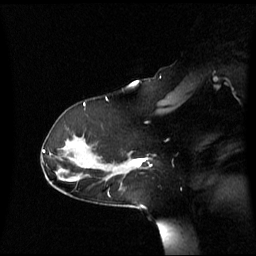
Breast MRI (dynamic contrast-enhanced), one sagittal slice; slice 41 of 60 in the series (ordered by position); dynamic contrast-enhanced series, image 2 of 3 at this slice position (ordered by acquisition); 1.5 T; TE 4.2 ms, TR 8.4 ms; 2.6 mm slice thickness; 256 × 256 image matrix, field of view 270 × 270 mm. Patient: female, 39 years. From the clinical record (not read from this slice): setting: breast cancer imaged before/during neoadjuvant chemotherapy; receptor status: triple-negative.
Annotated regions visible in this slice (semi-automatically segmented with operator editing):
- analysis volume of interest (the breast-tissue region the enhancement analysis was run in; not a lesion): bounding box (x1, y1, x2, y2) in pixels: (117, 152, 152, 176)
- tumour enhancement mask (voxels above the 70 % enhancement threshold inside the analysis volume of interest): (131, 158, 152, 167)